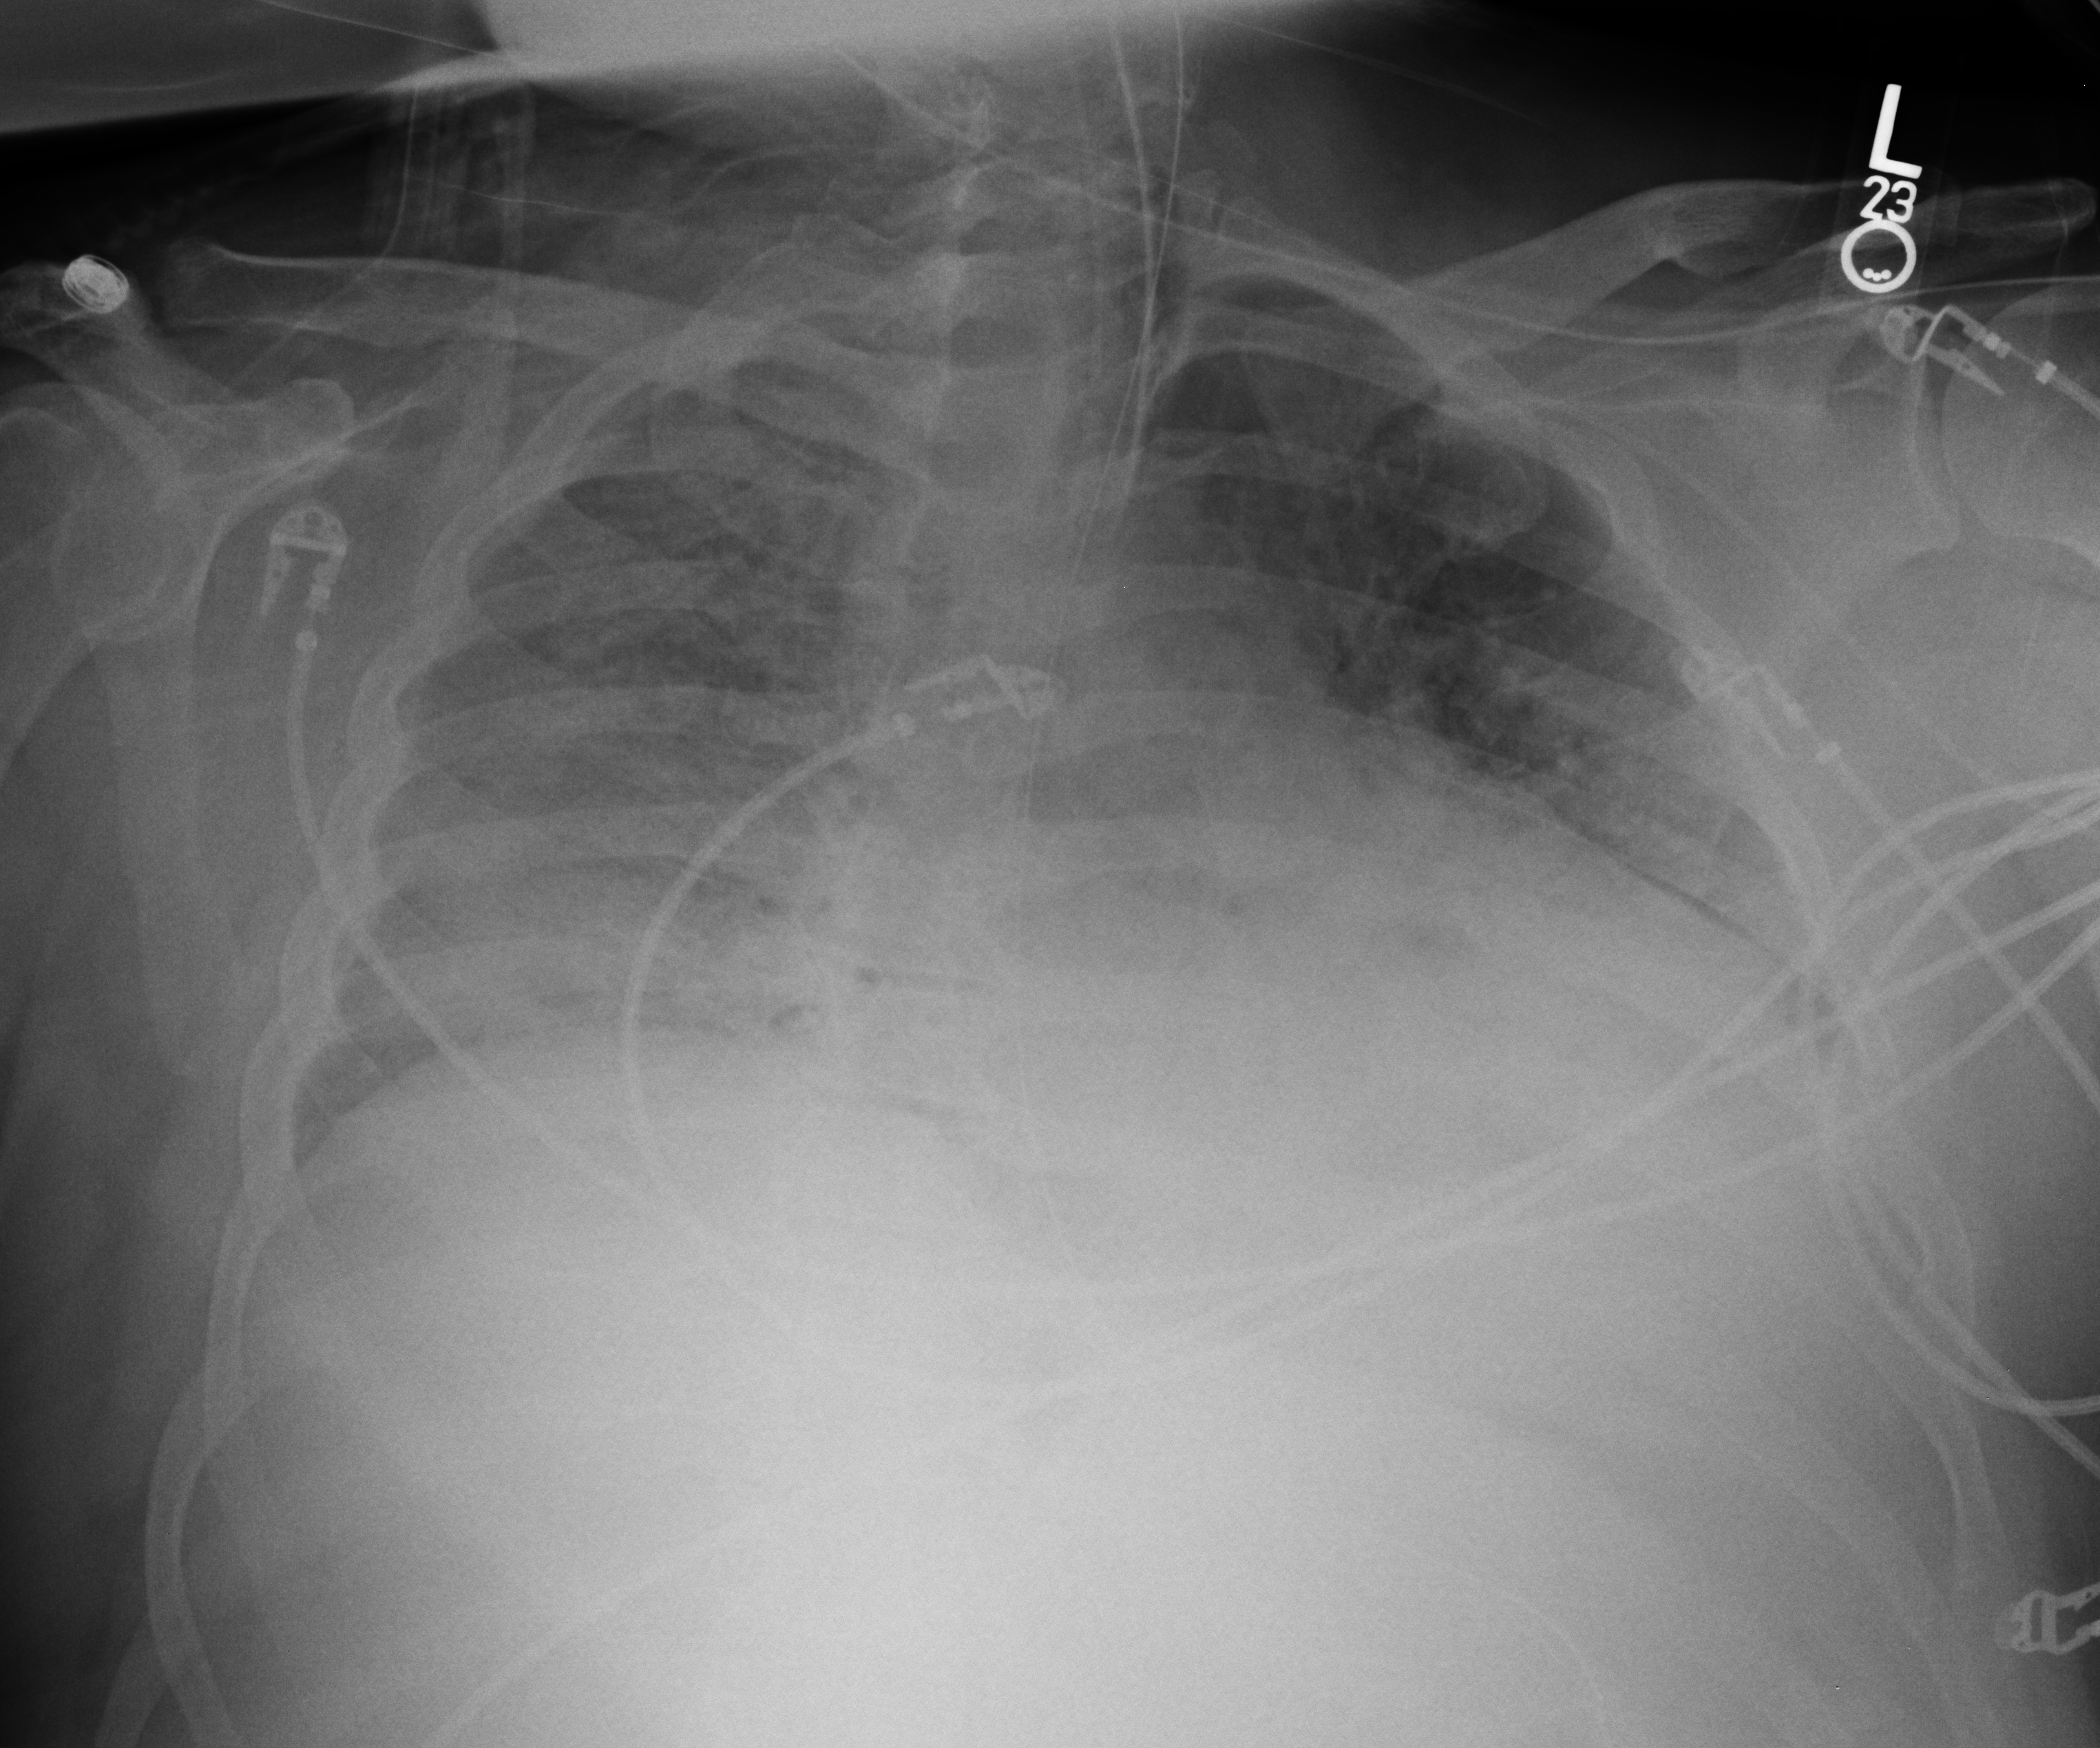
Chest X-ray (portable), anteroposterior (AP) projection. Patient hospitalised with COVID-19; male, aged 18–59 years.
From the hospital-stay record, not from the radiograph (when in the stay this image was taken is not recorded):
- admitted to intensive care during this hospital stay: yes
- length of hospital stay: 80 days